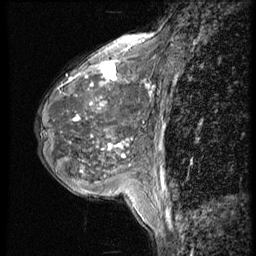
Breast MRI (dynamic contrast-enhanced), one sagittal slice; slice 18 of 56 in the series (ordered by position); 4 images stored at this slice position (order not interpretable as contrast timing); 1.5 T; TE 4.2 ms, TR 9 ms; 2.5 mm slice thickness; 256 × 256 image matrix, field of view 180 × 180 mm. Female patient, age 50 years. From the clinical record (not read from this slice): setting: breast cancer imaged before/during neoadjuvant chemotherapy; receptor status: triple-negative.
Structures marked on this image (semi-automatic segmentation, software-assisted and operator-edited):
- analysis volume of interest (the breast-tissue region the enhancement analysis was run in; not a lesion): bounding box [x1, y1, x2, y2] px = [34, 46, 148, 188]
- tumour enhancement mask (voxels above the 140 % enhancement threshold inside the analysis volume of interest): [92, 63, 146, 158]